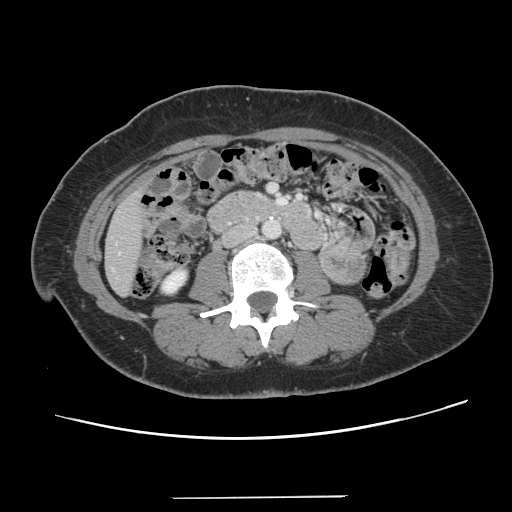
Contrast-enhanced abdominal CT, one axial slice; position 29 of 141 along the scan axis; intravenous contrast given; soft-tissue window (W 400 / L 40 HU); 2.5 mm slice thickness; 512 × 512 image matrix, field of view 366 × 366 mm. Female patient, age 53 years. Case-level facts recorded for this patient, not image findings: diagnosis: colorectal cancer liver metastases, imaged before liver resection; multiple liver metastases: no; largest metastasis: 14.5 cm; disease in both lobes: yes.
Structures marked on this image (expert manual segmentation):
- liver: bounding box (x1, y1, x2, y2) in pixels: (106, 195, 143, 294)
- planned liver remnant (the part of the liver to remain after resection): (106, 205, 143, 294)